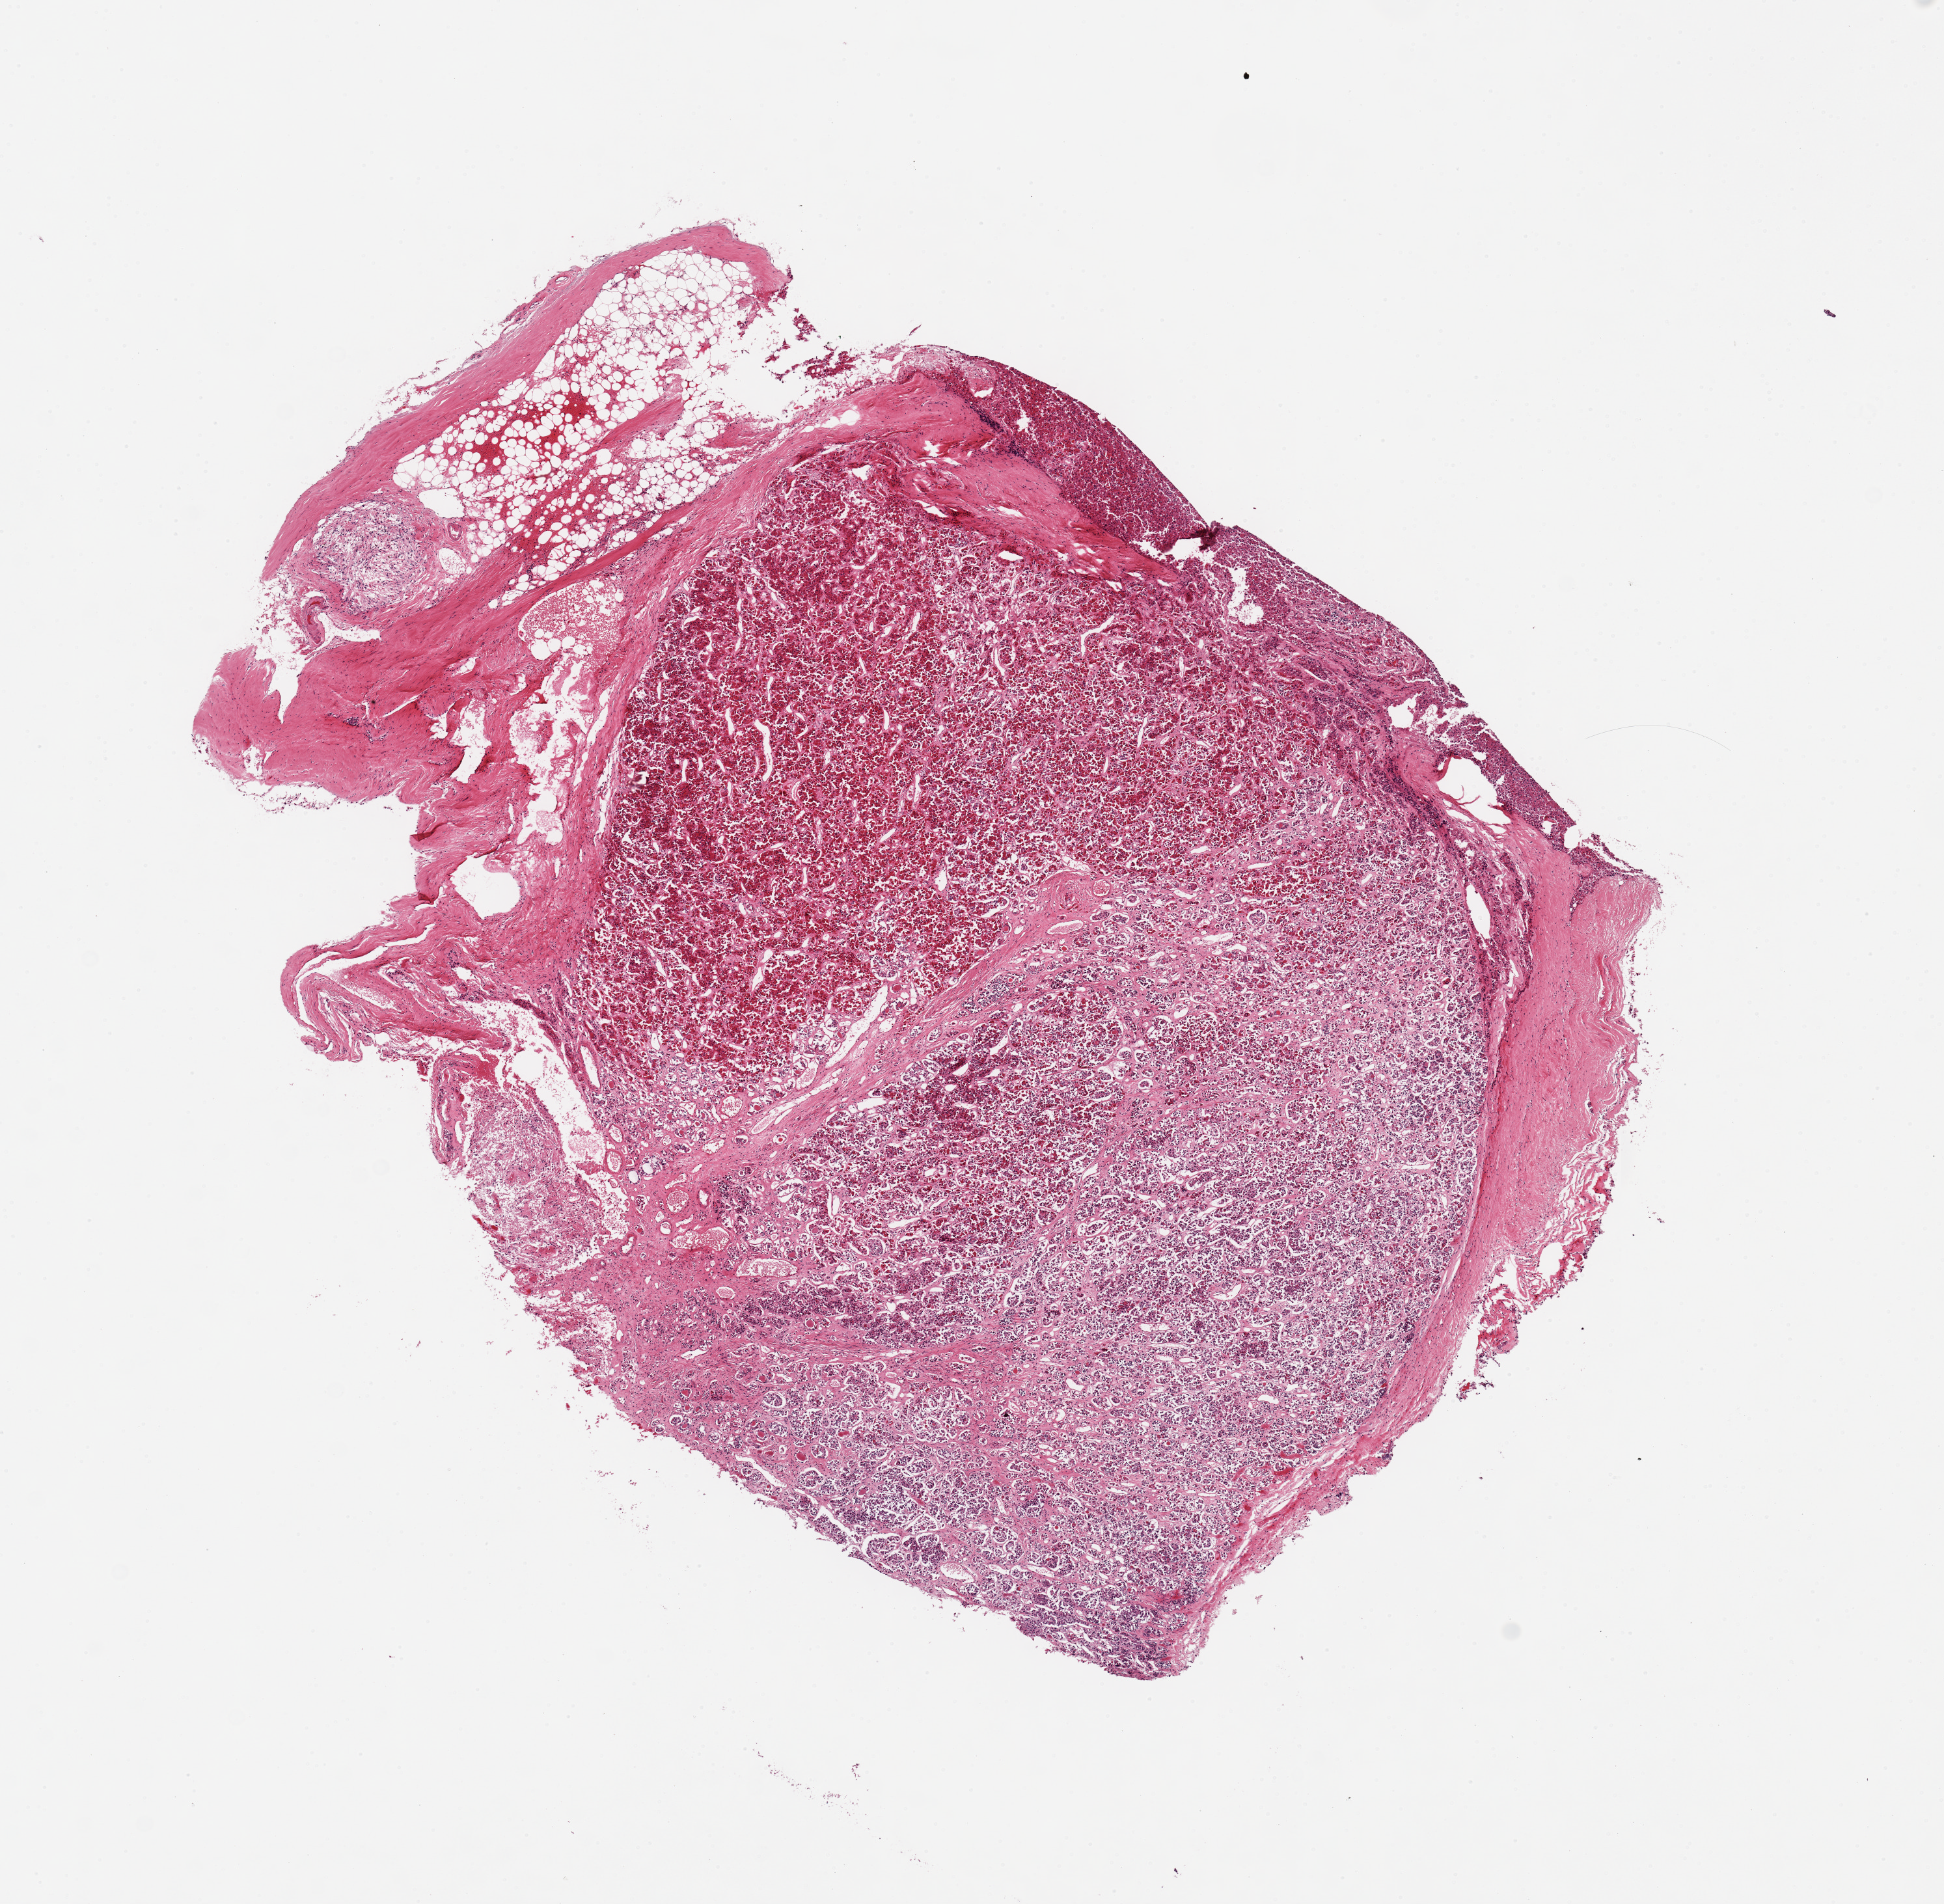
H&E whole-slide image, whole scanned area (about 11.8 x 11.6 mm, acquisition: 20x scan) shown as a low-resolution overview. PAXgene-fixed, paraffin-embedded tissue. Target tissue: pituitary. Tissue donor sample. Donor sex: male.
Reviewer comment on this tissue sample: 1 piece, ~50% adenohypophysis, 50% neurohypophysis; discontinuous adherent rim of fibrous tissue, ~1mm.